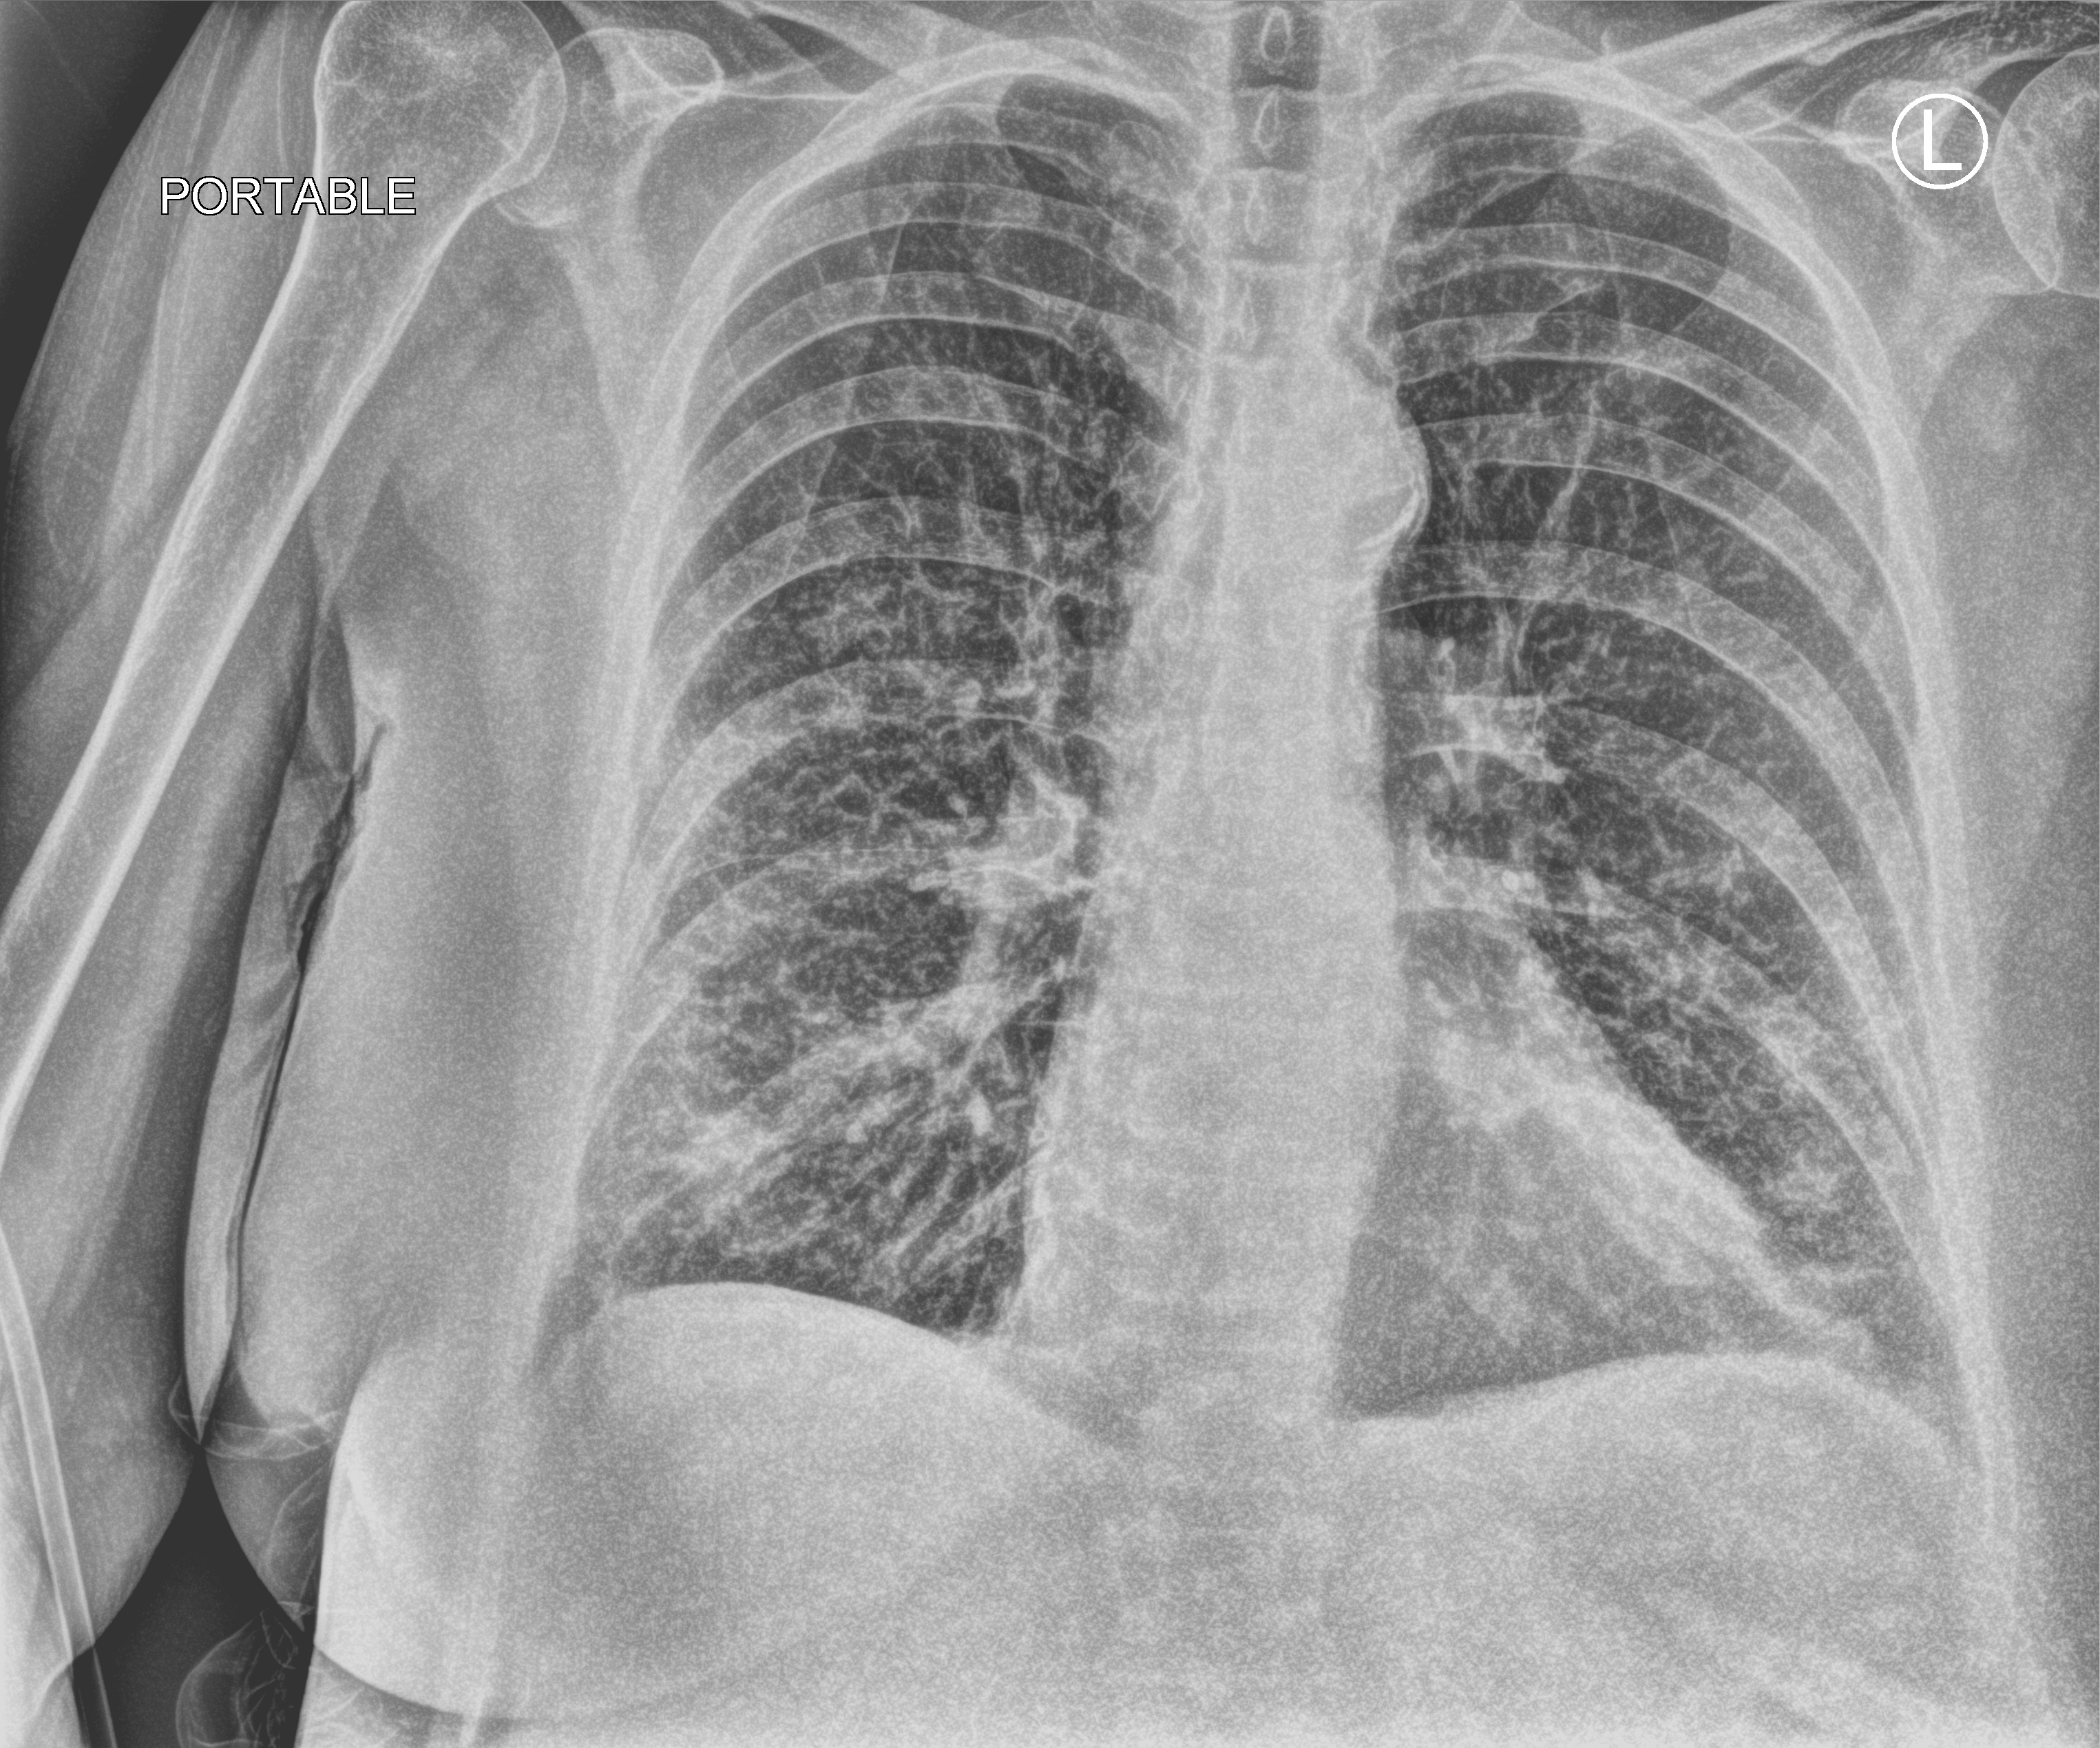
Chest X-ray (portable), anteroposterior (AP) projection. Patient hospitalised with COVID-19; female, aged 60–74 years.
Admission-level facts for this patient (not findings on this image; timing relative to this image not recorded): mechanically ventilated during this hospital stay: no; chronic kidney disease (admission record): no.